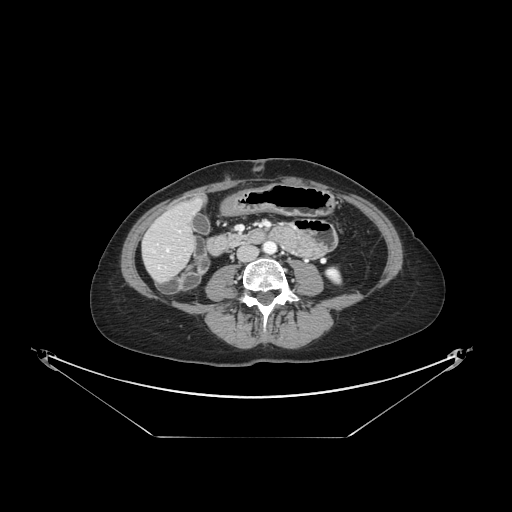
Contrast-enhanced abdominal CT, one axial slice. Slice 34 of 148 in the series (ordered by position). Reconstruction kernel STANDARD. Intravenous contrast given. Soft-tissue window (W 400 / L 40 HU). 2.5 mm slice thickness. 512 × 512 image matrix. Female patient, age 73 years. From the clinical record (not read from this slice): diagnosis: colorectal cancer liver metastases, imaged before liver resection; multiple liver metastases: no; largest metastasis: 1 cm; chemotherapy before resection: yes.
Structures marked on this image (manually delineated by an expert):
- hepatic veins: box from (x=167, y=249) to (x=169, y=252) px
- liver: (x=144, y=202)–(x=199, y=281)
- planned liver remnant (the part of the liver to remain after resection): (x=162, y=202)–(x=199, y=239)